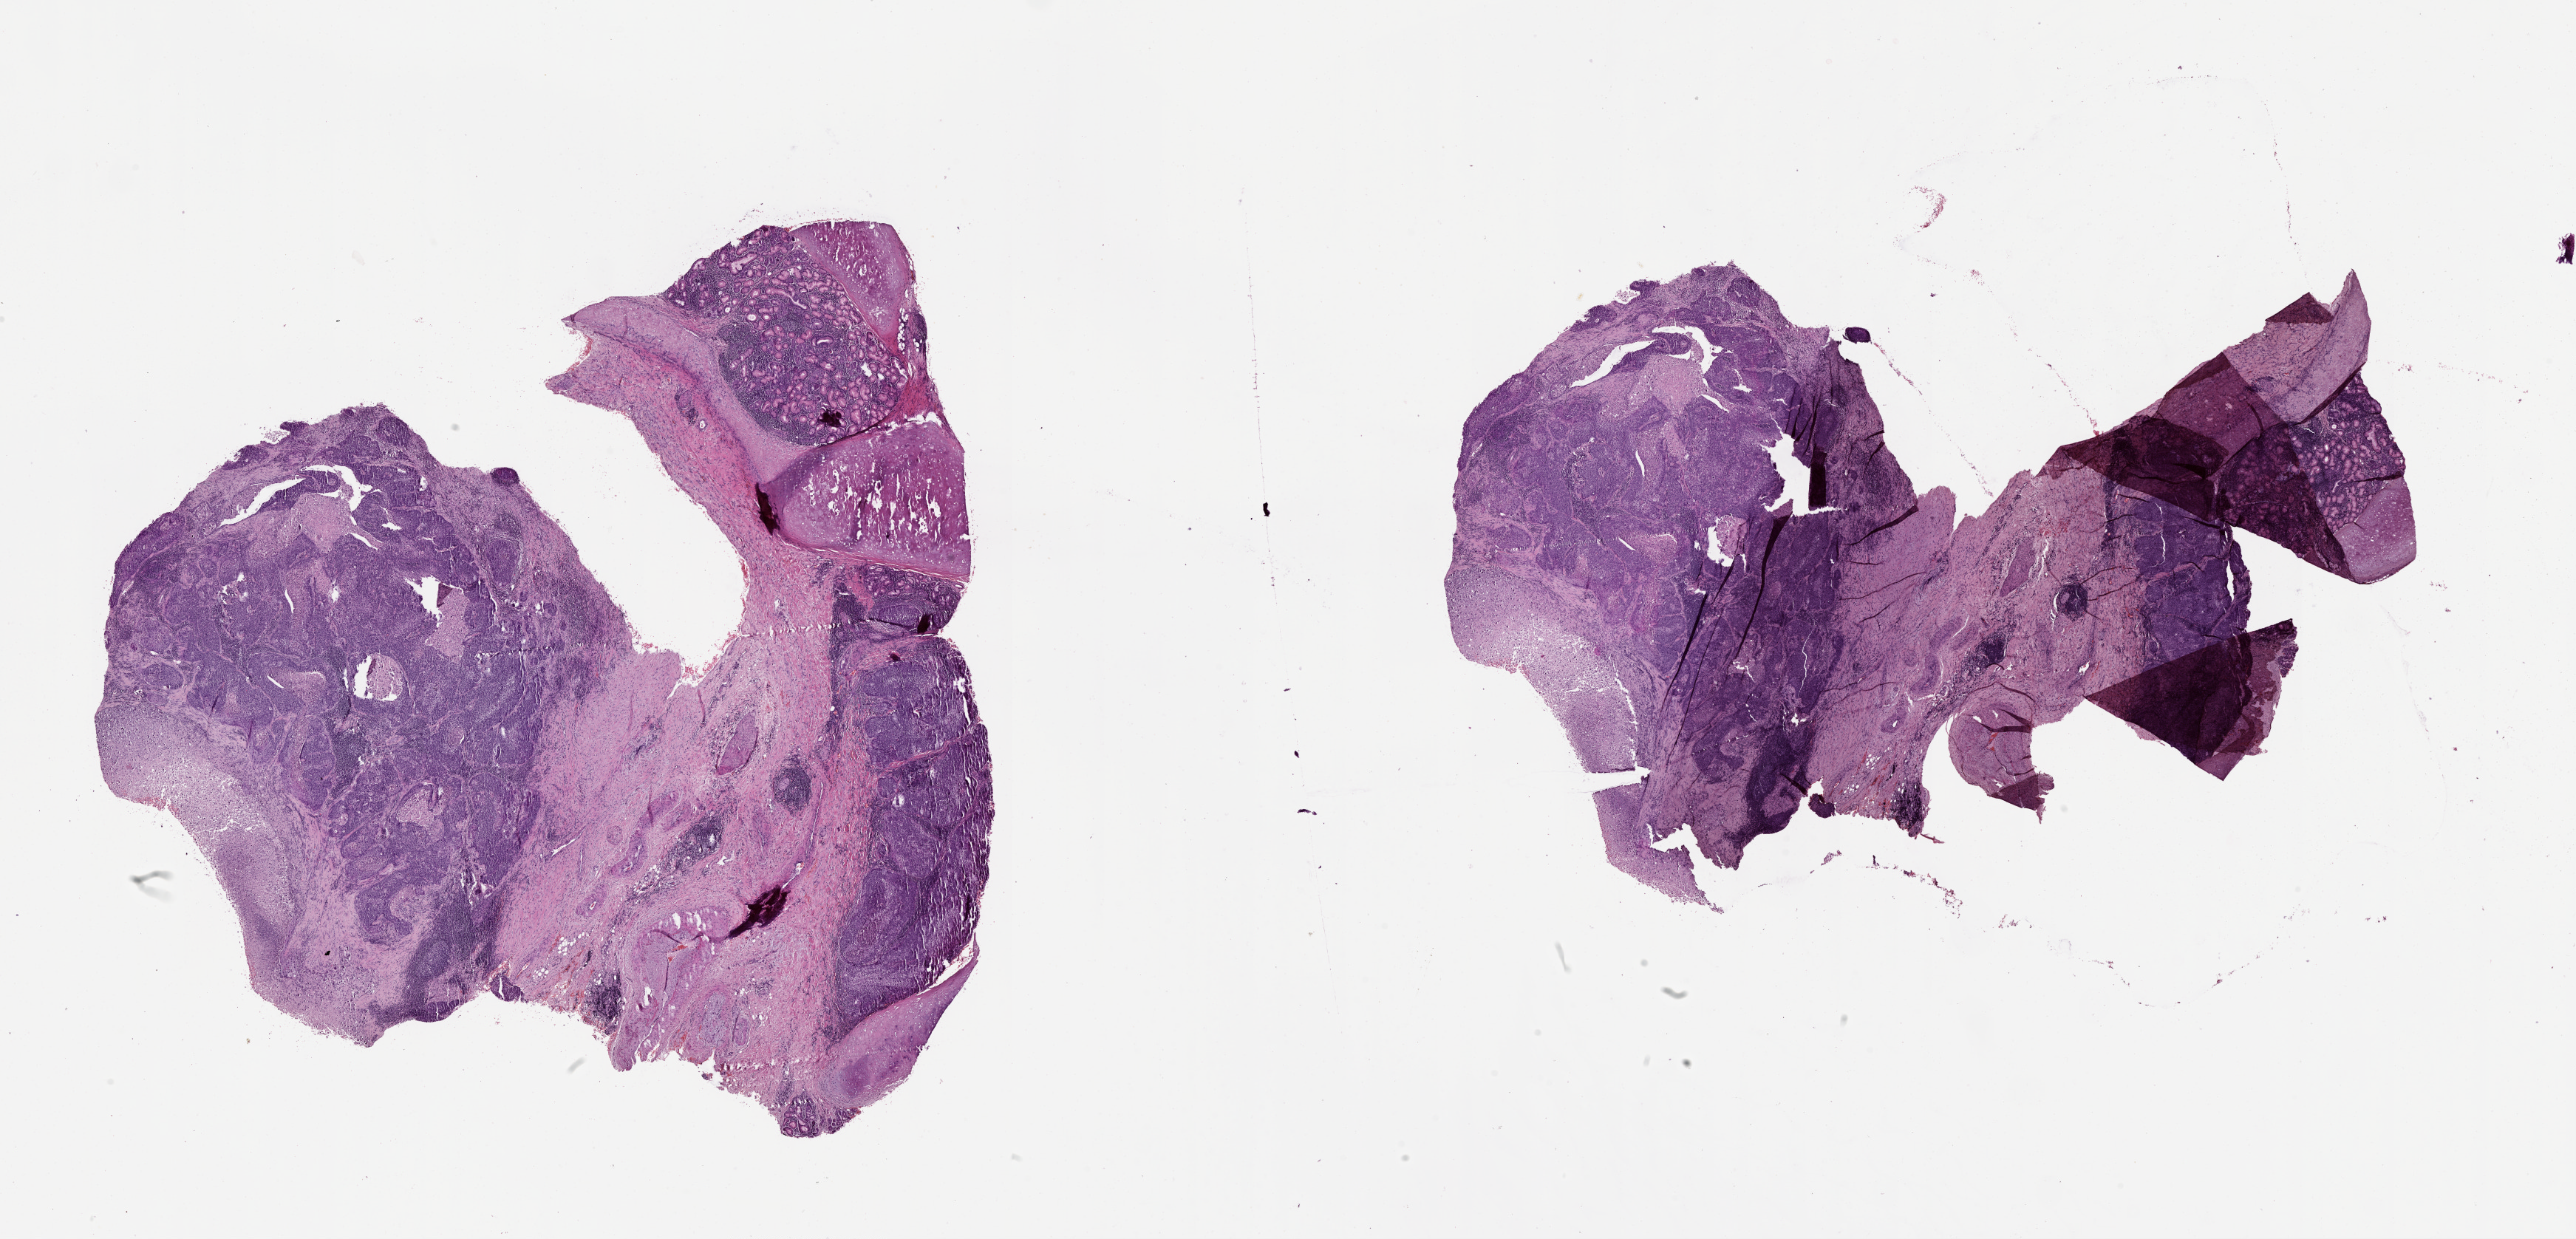
Digitized H&E tissue section (whole slide), whole scanned area (about 28.1 x 13.5 mm) shown as a low-resolution overview, lung, tumour tissue. Patient: male, age 53 years.
Patient diagnosis (cohort enrolment): squamous cell carcinoma (lung).